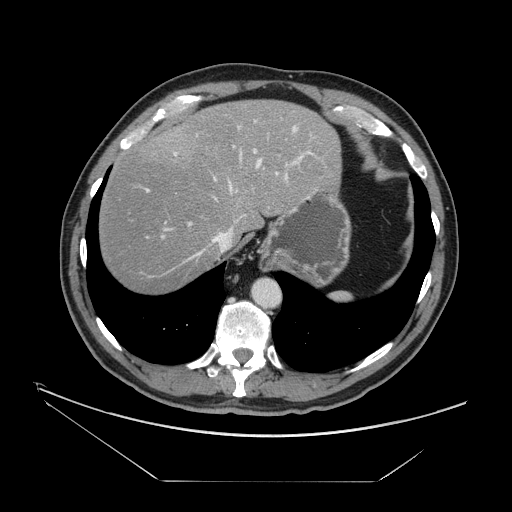
Contrast-enhanced abdominal CT, one axial slice. 120 kVp. Soft-tissue window (W 400 / L 40 HU). 2.5 mm slice thickness. 512 × 512 image matrix, field of view 440 × 440 mm. Male patient, age 65 years. Case-level facts recorded for this patient, not image findings: diagnosis: colorectal cancer liver metastases, imaged before liver resection; multiple liver metastases: yes; largest metastasis: 4.2 cm.
Structures marked on this image (expert manual segmentation):
- hepatic veins: bounding box (x1, y1, x2, y2) in pixels: (188, 126, 297, 260)
- liver: (98, 100, 340, 293)
- planned liver remnant (the part of the liver to remain after resection): (98, 100, 340, 294)
- portal vein (with intrahepatic branches): (144, 118, 312, 239)